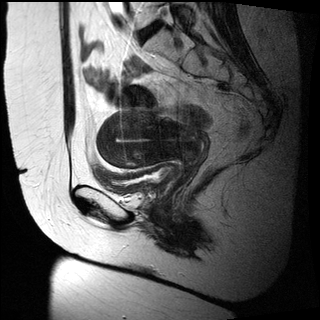
Pelvic MRI for cervical cancer, one sagittal slice. Slice 17 of 27 in the series (ordered by position). T2-weighted. 1.5 T. TE 89 ms, TR 2740 ms. 4 mm slice thickness. 320 × 320 image matrix, field of view 260 × 260 mm. Patient: female, 47 years.
Structures marked on this image (manually delineated by an expert):
- uterus and cervix: bounding box [x1, y1, x2, y2] px = [96, 111, 201, 169]